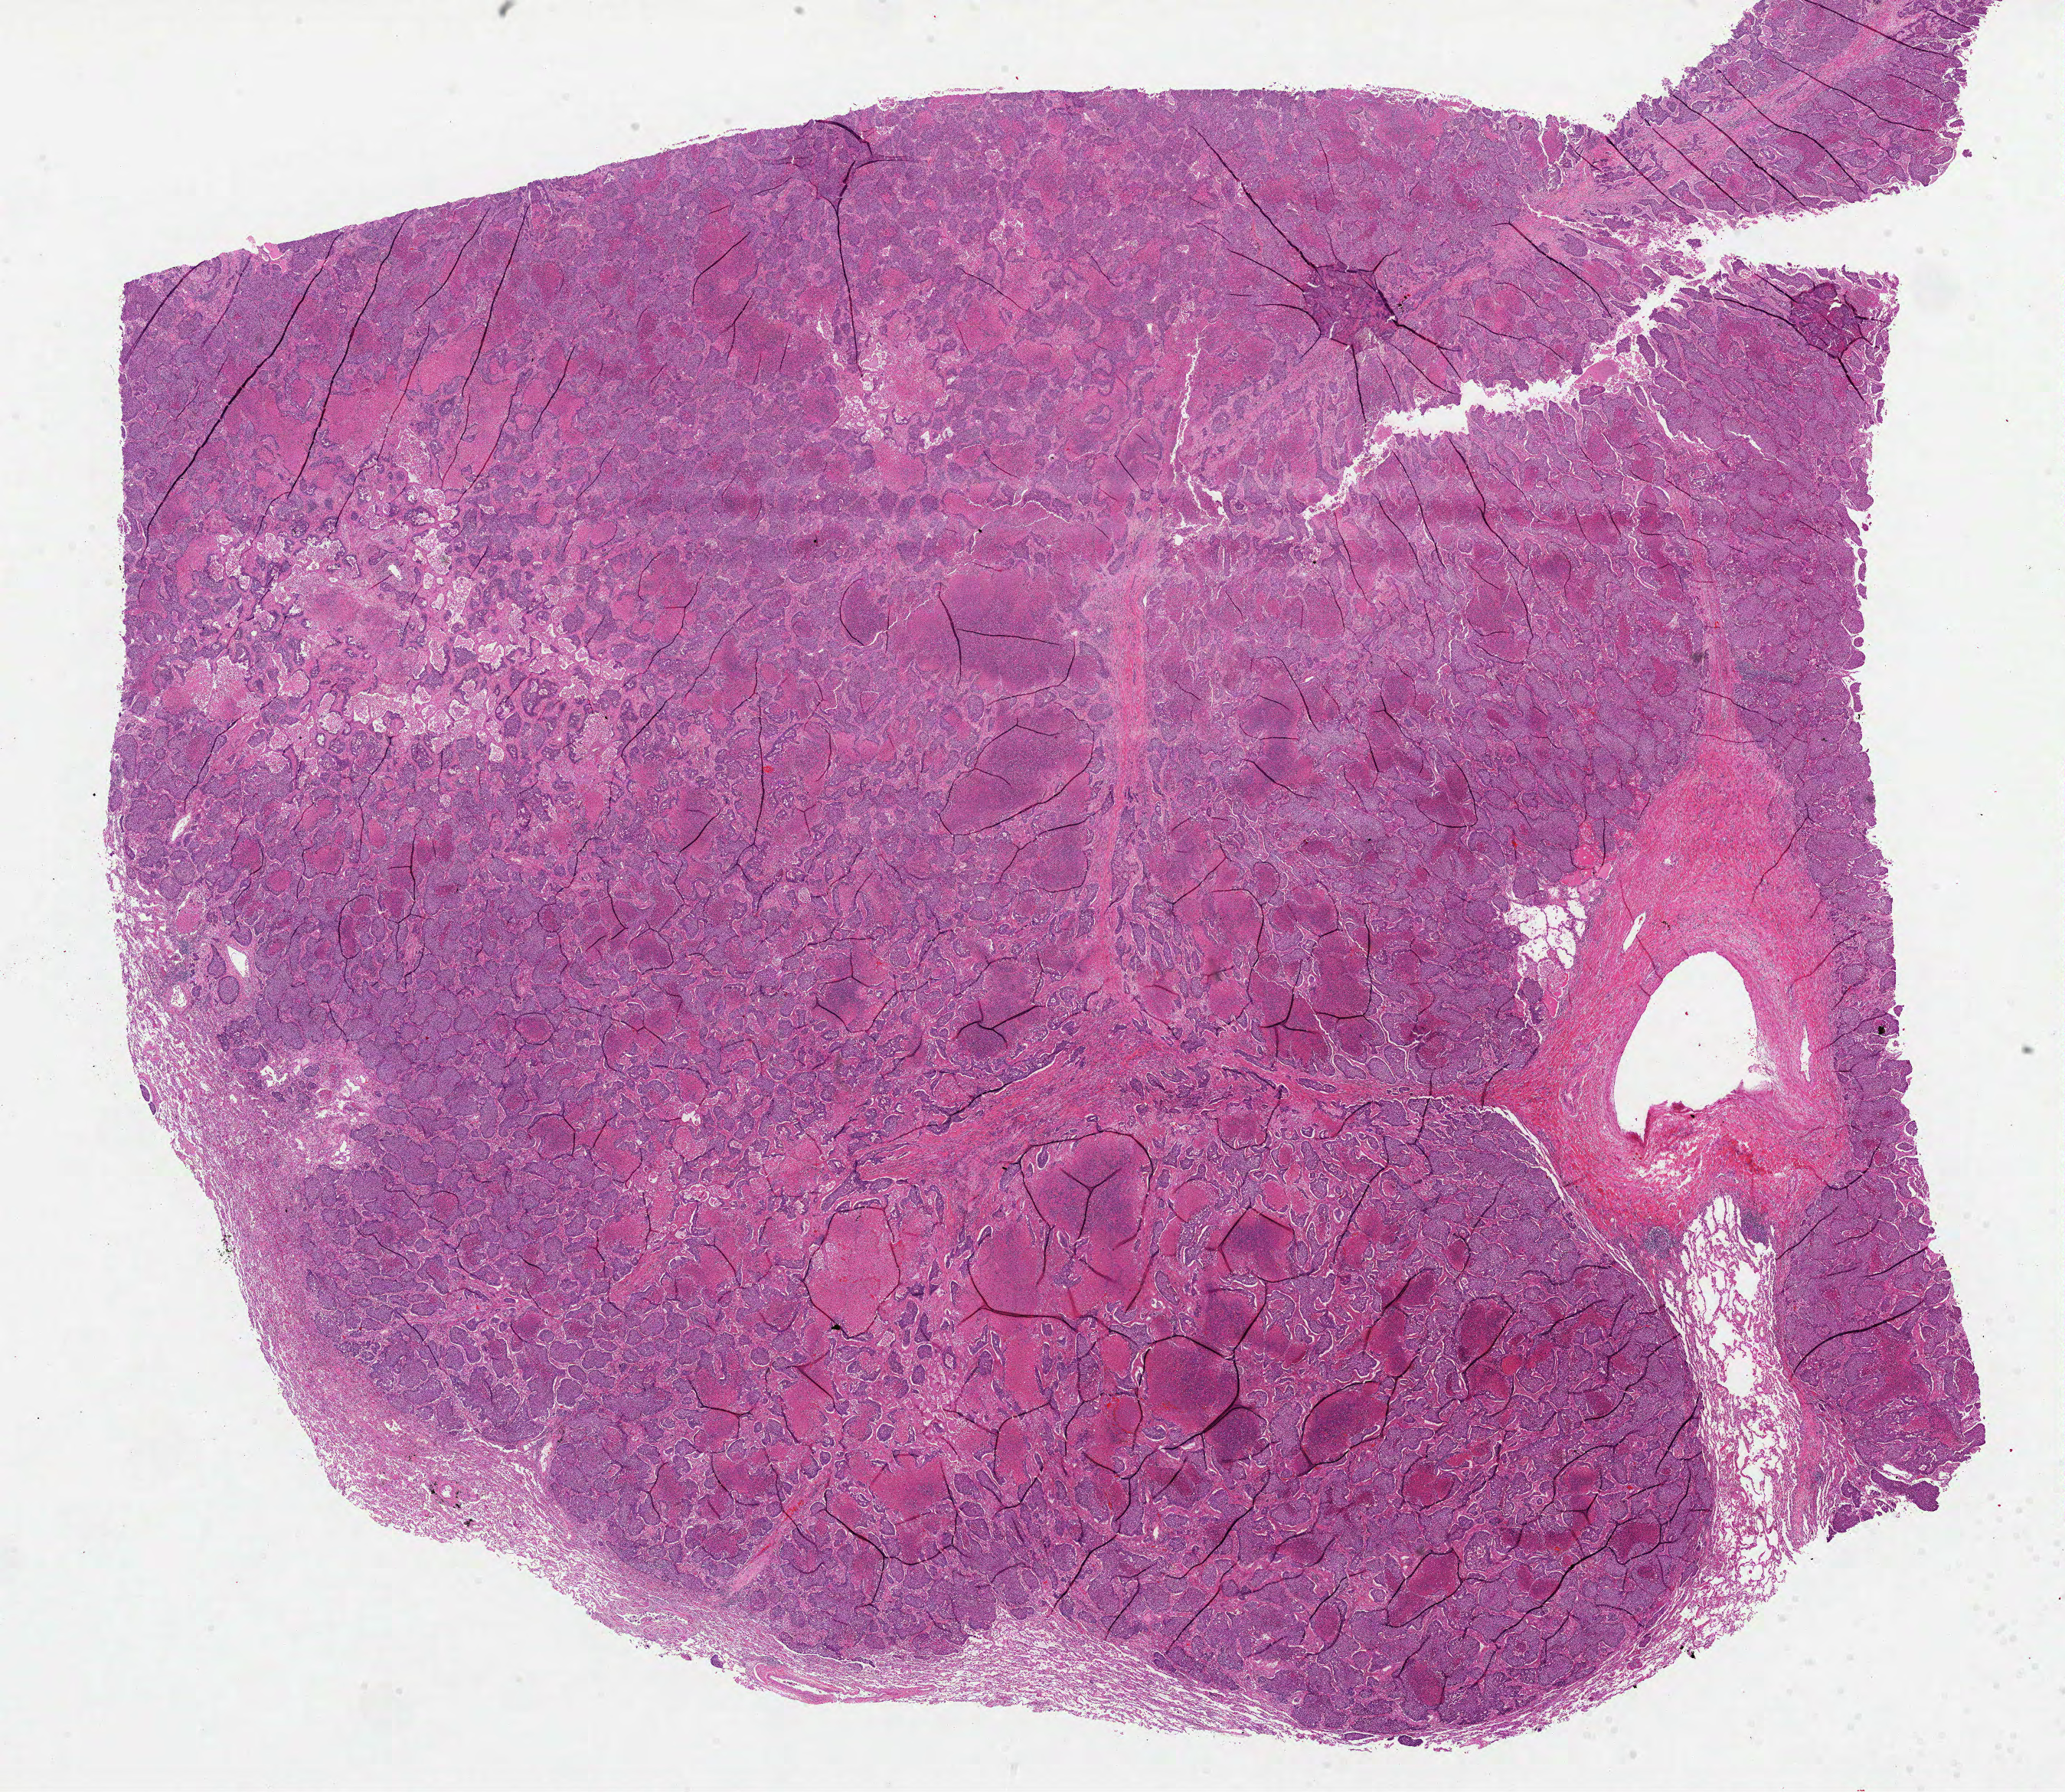
Whole-slide histology image, Hematoxylin and eosin (H&E) stained, shown as a low-resolution overview of the whole scanned area (about 21.8 x 18.9 mm). Formalin-fixed paraffin-embedded (FFPE) diagnostic section. Sample: primary tumour, lung. Male, age 57 years at initial diagnosis.
Diagnosis: Squamous cell carcinoma, NOS.